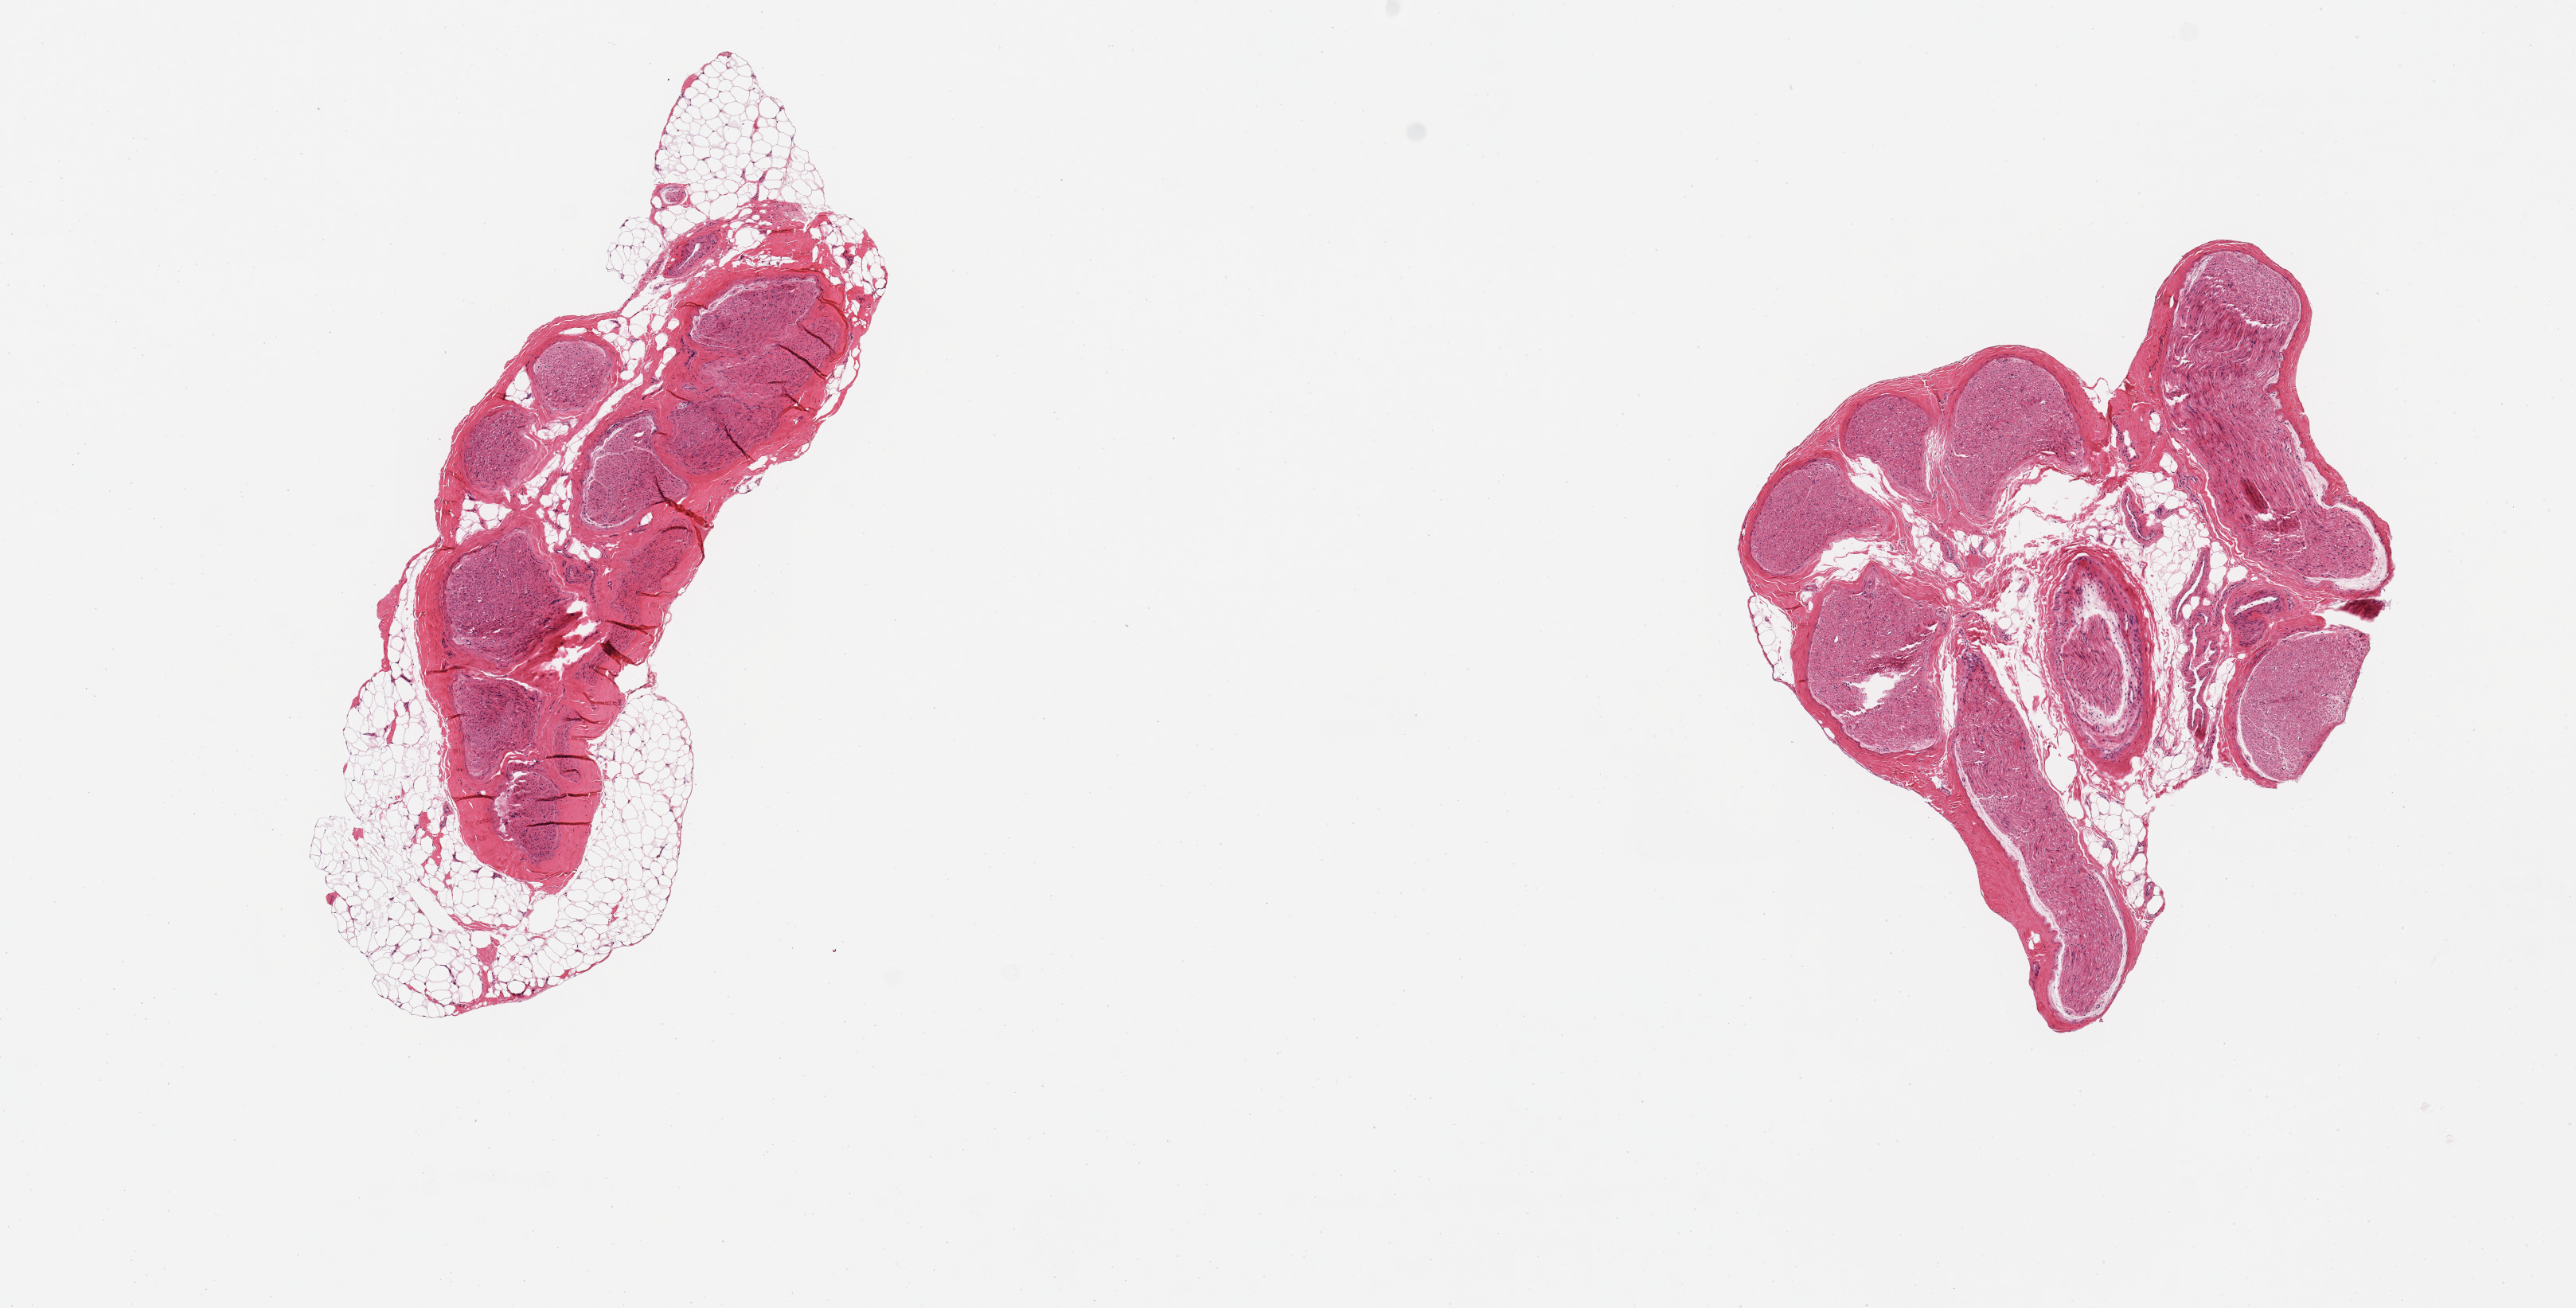
Digitized haematoxylin and eosin-stained section — low-resolution overview of the scanned area, about 12.8 x 6.5 mm (from a 20x scan); PAXgene-fixed paraffin-embedded (PFPE) section; sampled site (target tissue): tibial nerve; tissue donor sample. Male donor.
* pathologist's review note for this sample: 2 pieces; 30% internal & external fat